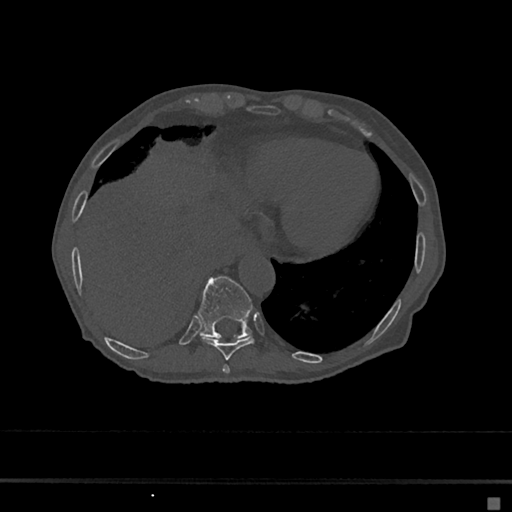
CT including the spine, one axial slice; slice 252 of 797 in the series (ordered by position); reconstruction kernel Br40s/3; 120 kVp; bone window (W 1800 / L 400 HU); 0.5 mm slice thickness; 512 × 512 image matrix, field of view 360 × 360 mm. Female patient, age 68 years. Case-level facts recorded for this patient, not image findings: primary cancer: renal.
Annotated regions visible in this slice (semi-automatically segmented with operator editing):
- T10 vertebra: box from (x=198, y=276) to (x=253, y=339) px
- T8 vertebra: (x=222, y=365)–(x=230, y=374)
- T9 vertebra: (x=200, y=337)–(x=255, y=360)